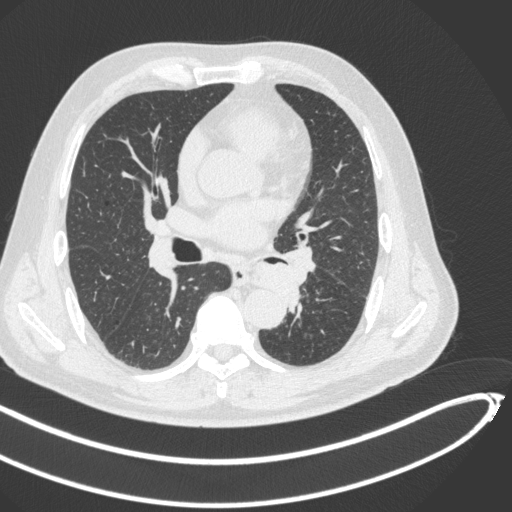
Chest CT, one axial slice. Lung window (W 1500 / L -600 HU). 1 mm slice thickness. 512 × 512 image matrix, field of view 400 × 400 mm. Patient: male, 64 years. From the clinical record (not read from this slice): clinical TNM (as recorded): T1c N0 M0.
Structures marked on this image (rectangle marked by the reading radiologist):
- lung tumour (recorded histology: squamous cell carcinoma): bounding box [x1, y1, x2, y2] px = [248, 251, 300, 311]